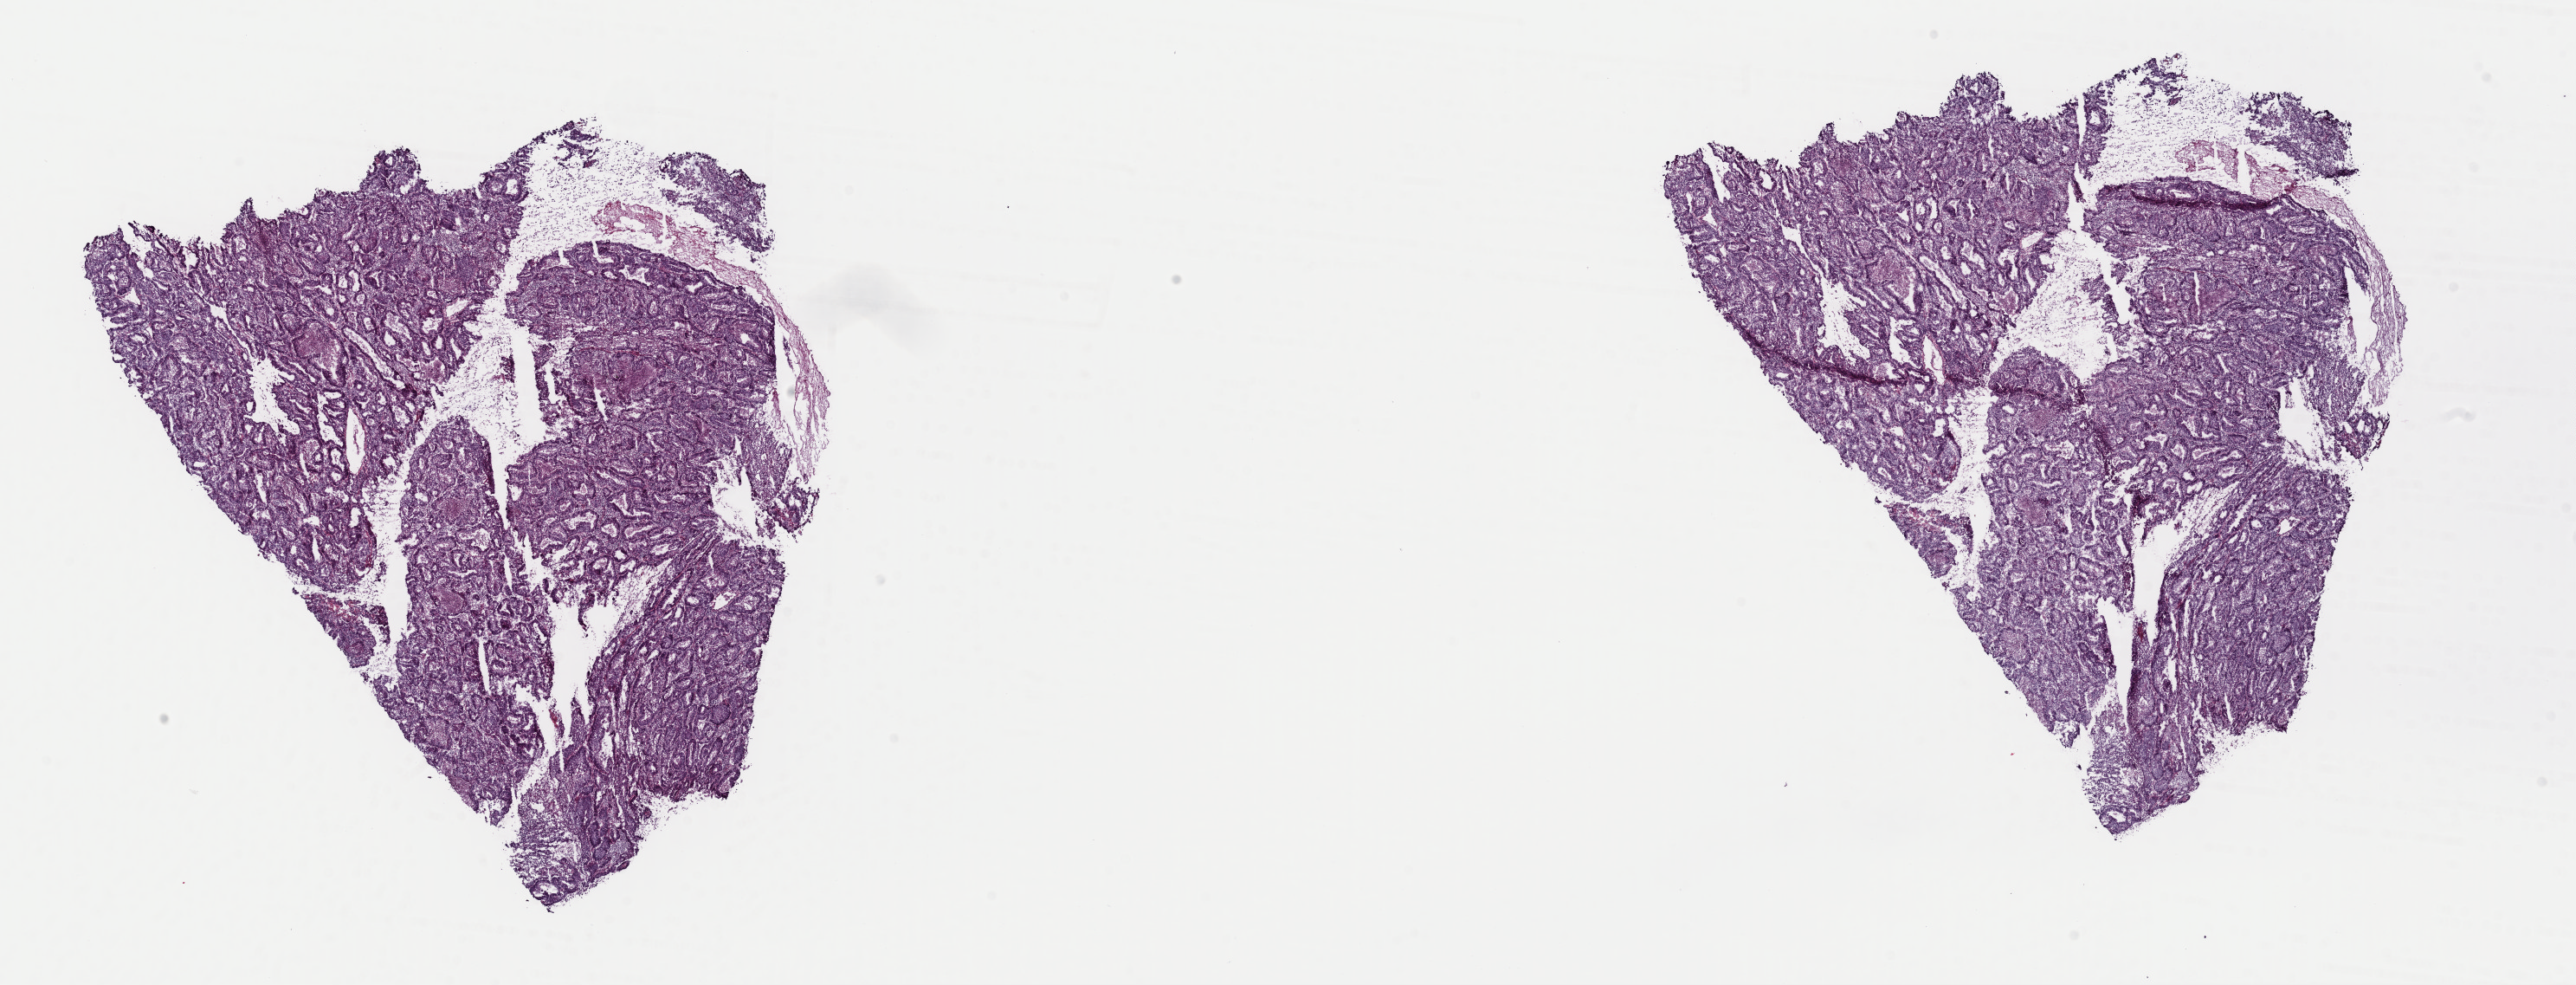
Whole-slide histology image, Hematoxylin and eosin (H&E) stained — low-resolution overview of the scanned area, about 23.5 x 9.0 mm, frozen section from the top of the tissue portion, sample: primary tumour, uterus. Female, age 65 years at initial diagnosis. Histologic grade: G3 (poorly differentiated). Slide review estimates, as recorded: tumour cells 90%, tumour nuclei 75%, normal cells 0%, stromal cells 0%, necrosis 10%. Infiltration values recorded for this section: lymphocyte infiltration 5%, monocyte infiltration 0%, neutrophil infiltration 0%.
Lymph nodes positive (case pathology): 0 of 5 examined. Histologic diagnosis: Endometrioid adenocarcinoma, NOS (endometrium). FIGO stage: IA.